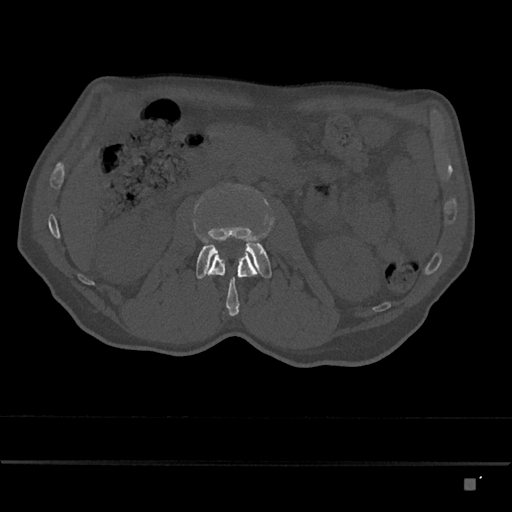
CT including the spine, one axial slice. Slice 440 of 797 in the series (ordered by position). 120 kVp. Bone window (W 1800 / L 400 HU). 0.5 mm slice thickness. 512 × 512 image matrix, field of view 390 × 390 mm. Male patient, age 72 years. From the clinical record (not read from this slice): primary cancer: prostate.
Structures marked on this image (semi-automatic segmentation, software-assisted and operator-edited):
- L2 vertebra: bounding box <204,250,257,316> (left, top, right, bottom; pixels)
- L3 vertebra: <196,186,272,279>